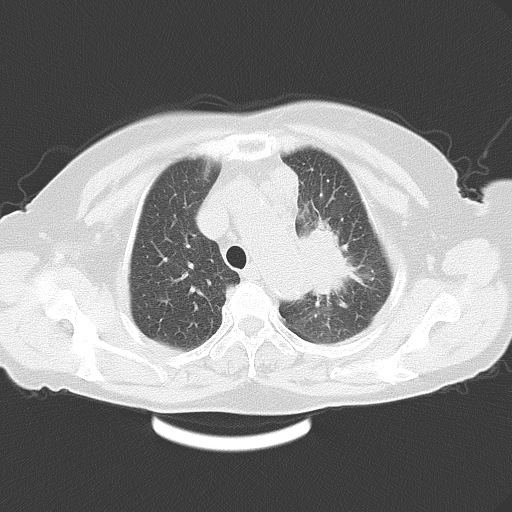
Chest CT, one axial slice; slice 42 of 54 in the series (ordered by position); reconstruction kernel B70f; 120 kVp; lung window (W 1500 / L -600 HU); 5 mm slice thickness; 512 × 512 image matrix, field of view 353 × 353 mm. Patient: female, 71 years. From the clinical record (not read from this slice): clinical TNM (as recorded): T3 N3 M0.
Annotated regions visible in this slice (rectangle marked by the reading radiologist):
- lung tumour (recorded histology: adenocarcinoma): box from (x=298, y=212) to (x=360, y=309) px